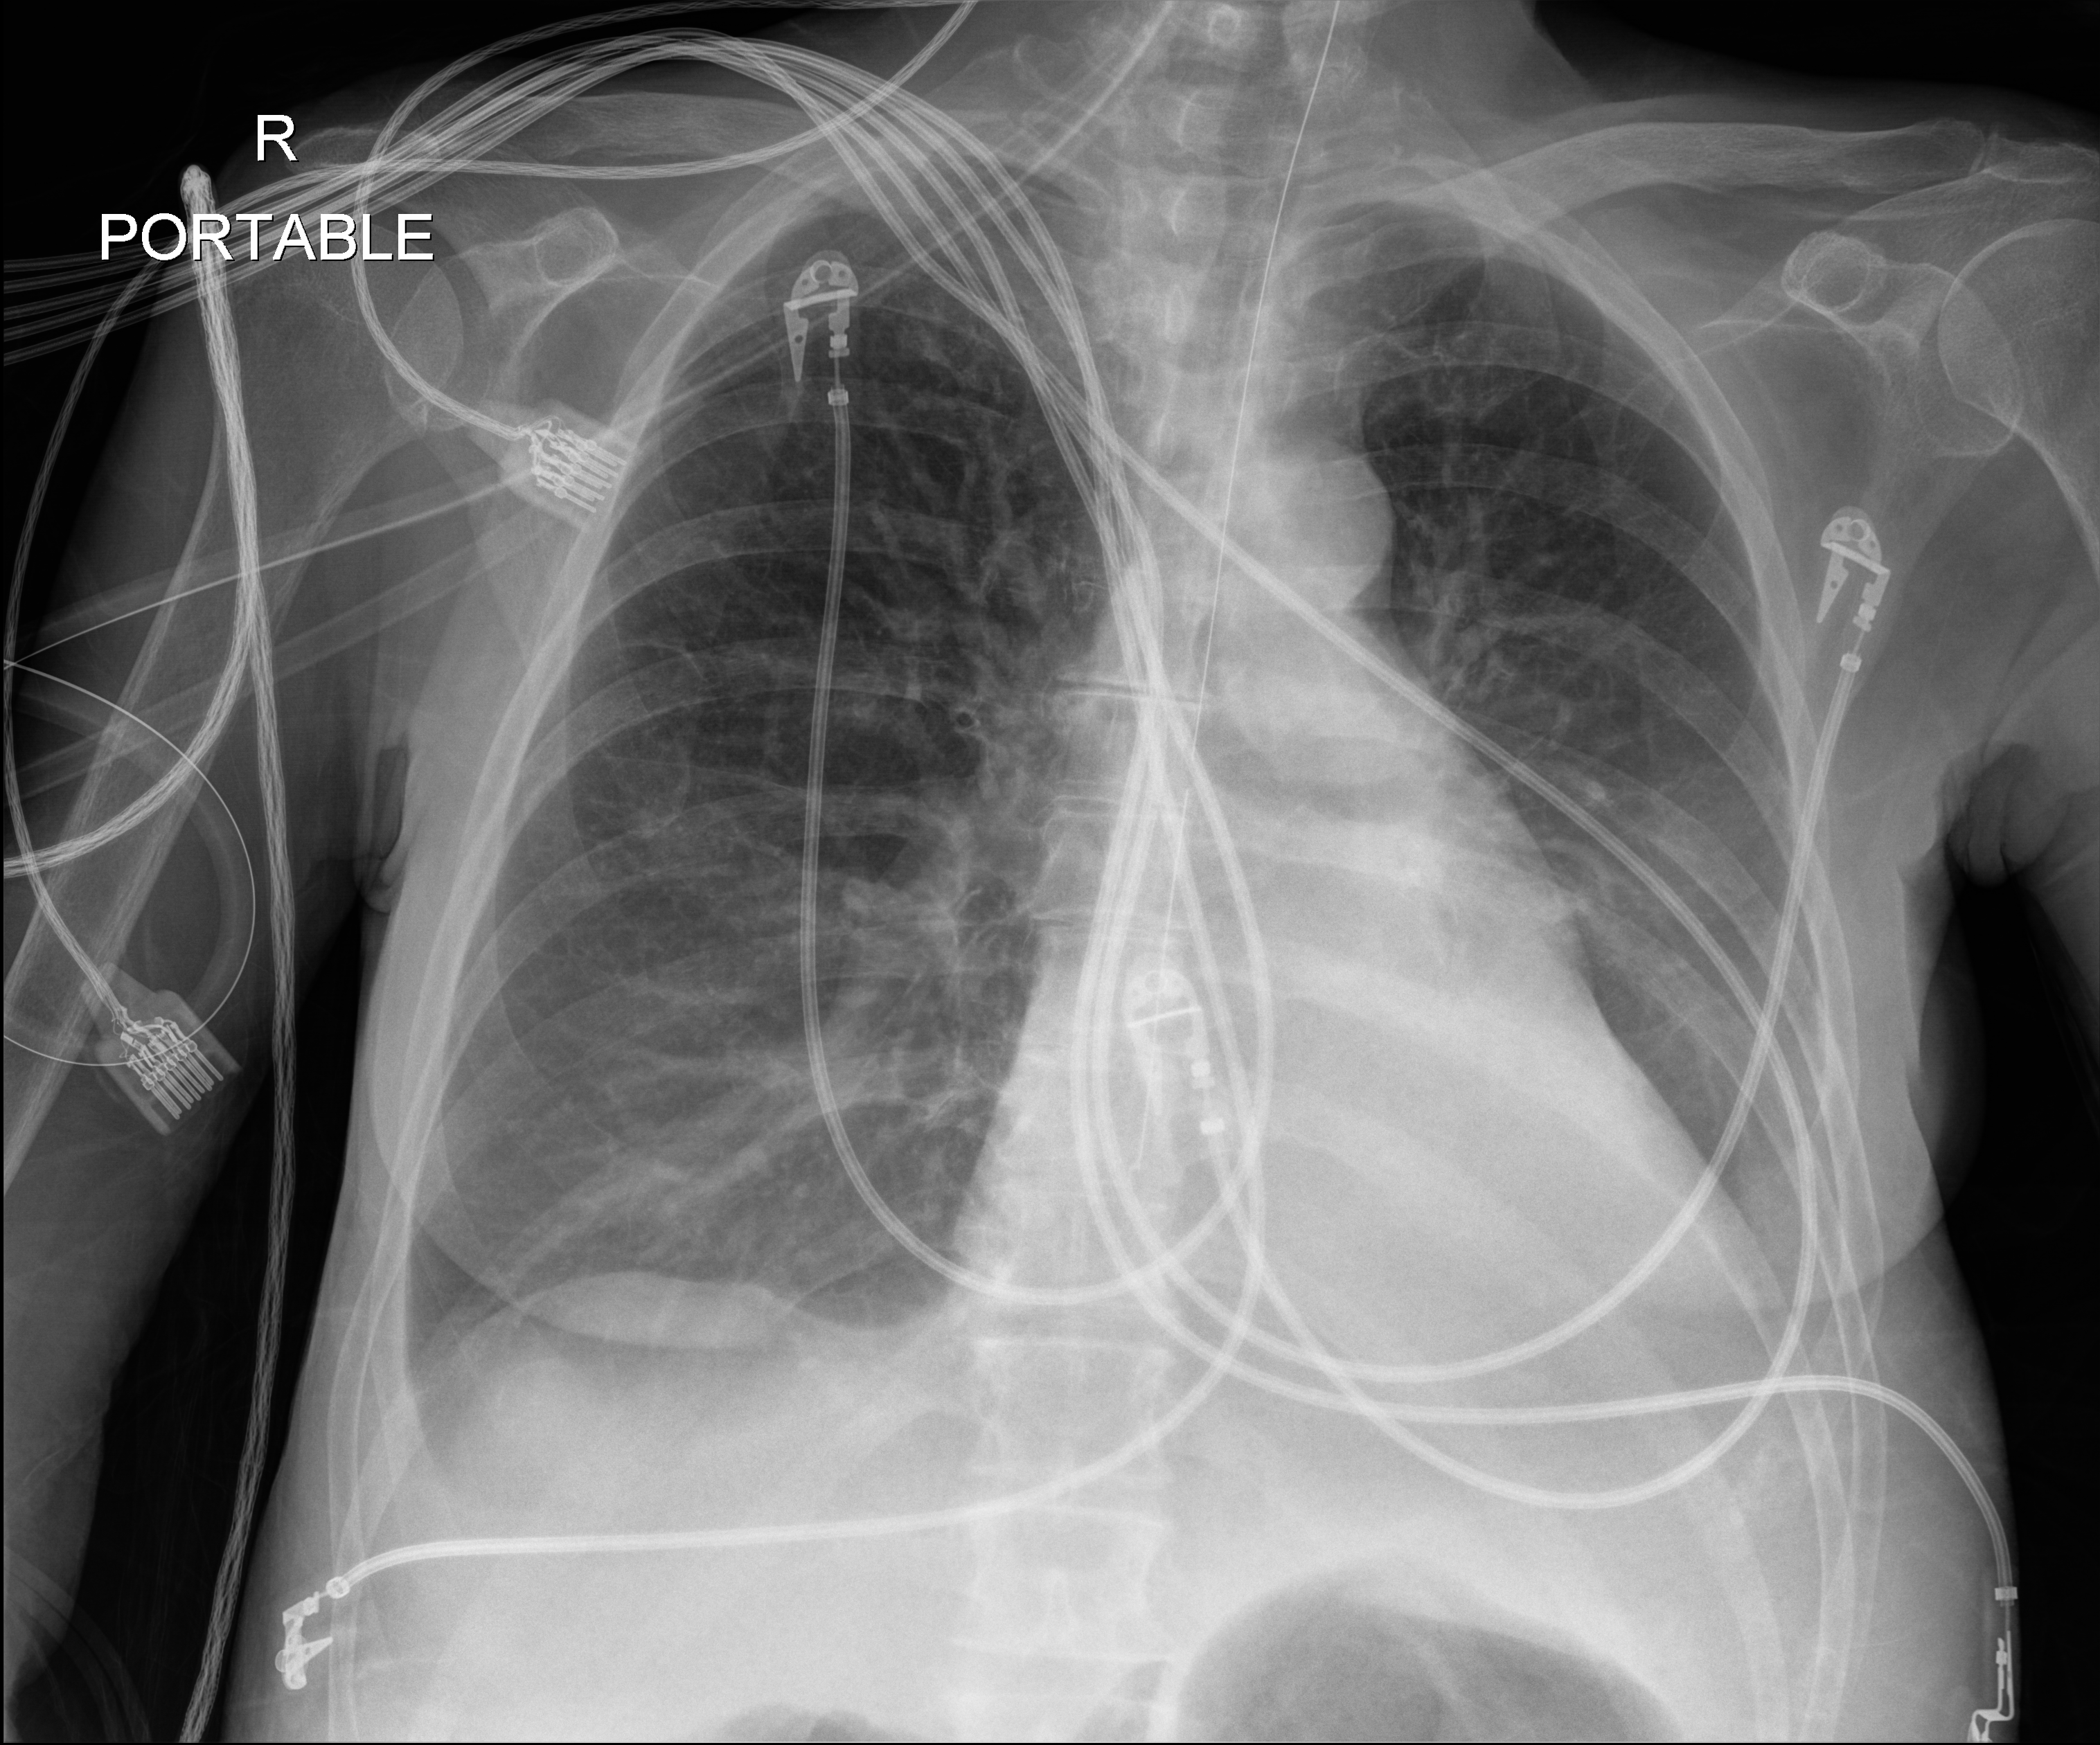
Bedside chest radiograph (digital radiography); anteroposterior (AP) projection. Female patient hospitalised with COVID-19, age 60–74 years.
Hospital-stay facts (about this admission, not read from this image; timing relative to this image not recorded):
- length of hospital stay: 38 days
- mechanically ventilated during this hospital stay: yes
- admitted to intensive care during this hospital stay: yes